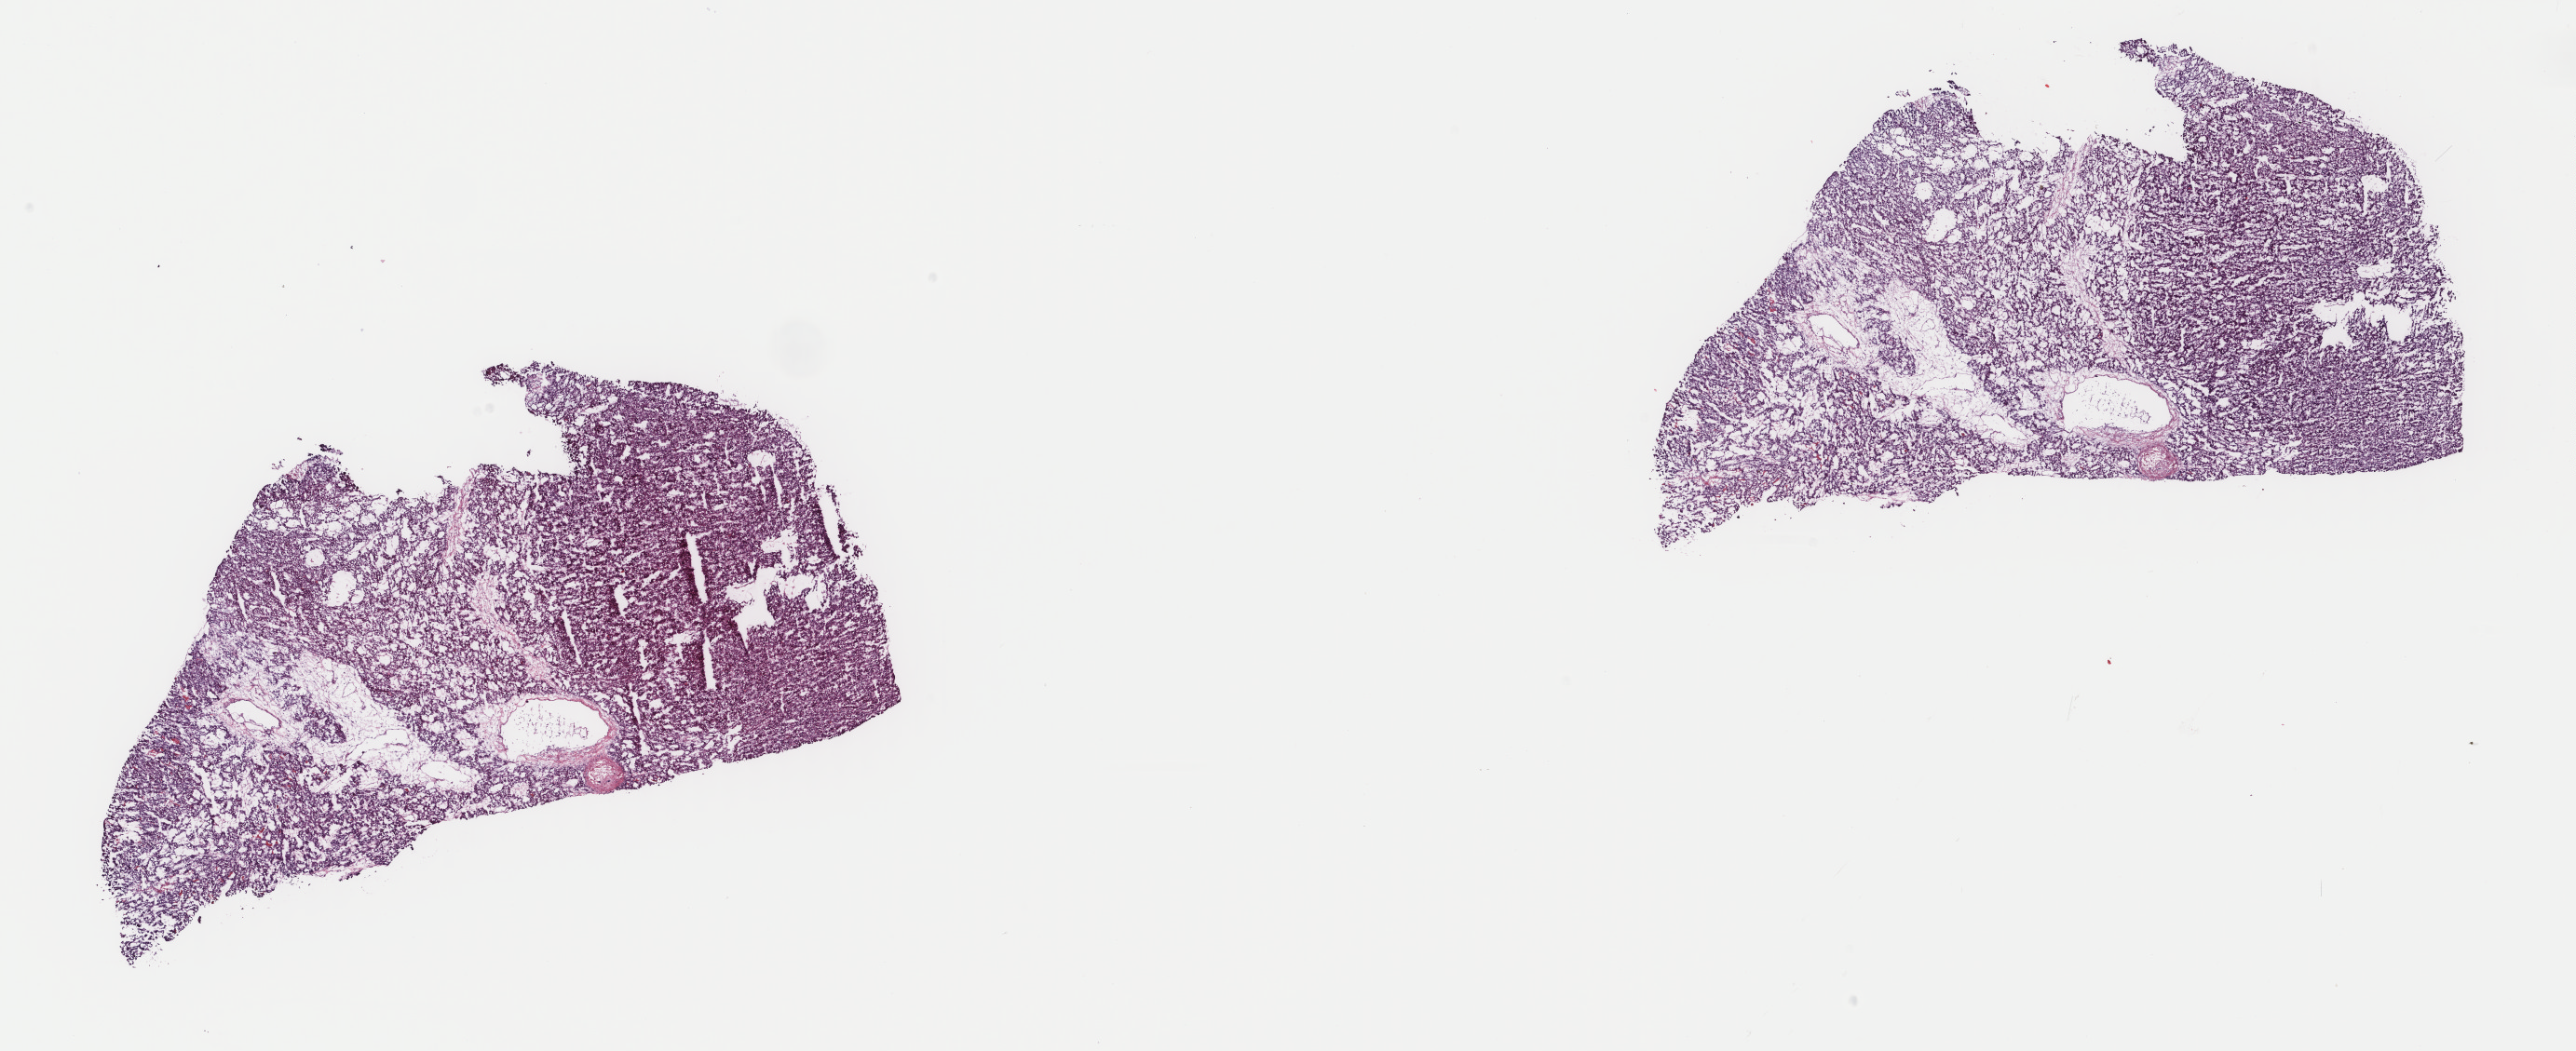
Digitized H&E tissue section (whole slide) — low-resolution overview of the scanned area, about 22.0 x 9.0 mm (slide scanned at 40x). Frozen section. Primary tumour sample from the liver. Patient: female, age at initial diagnosis 74 years. Histologic grade: G2 (moderately differentiated). Composition of this section per pathologist review: tumour cells 80%, tumour nuclei 90%, normal cells 0%, stromal cells 10%, necrosis 10%. Inflammatory infiltration, as recorded: lymphocyte infiltration 0%, monocyte infiltration 0%, neutrophil infiltration 0%.
Histologic diagnosis: Hepatocellular carcinoma, NOS. AJCC pathologic stage: IIIA (7th edition).